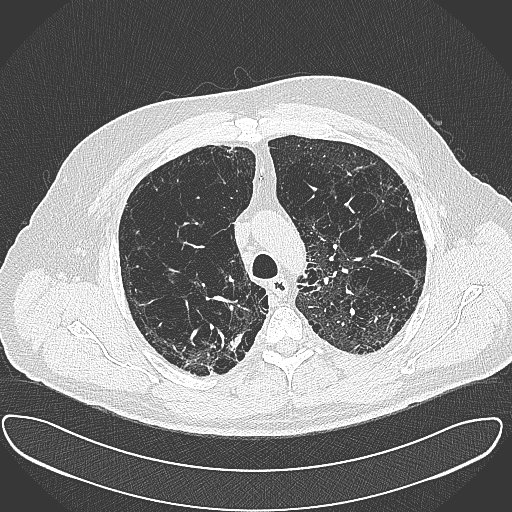
Chest CT (low-dose screening protocol), one axial image. Baseline annual screen. Lung window (W 1500 / L -600 HU). Slice 95 of 385 in the series. Male, age 60 years at enrolment.
• Expert reader's lesion annotation, box from (x=191, y=327) to (x=250, y=380) px.
• Reader record for this screening exam (exam-level; its link to the box is not recorded): non-calcified nodule or mass ≥4 mm, right upper lobe, 15 × 25 mm, spiculated (stellate) margins, soft tissue attenuation.
• Official screen result: positive, change unspecified: nodule(s) >= 4 mm or enlarging nodule(s), mass(es), or other non-specific abnormalities suspicious for lung cancer.
• Lung cancer was diagnosed 32 days after this screen: carcinoma, NOS, right upper lobe, moderately differentiated (G2), stage IB (AJCC 6th edition), 35 mm at pathology.